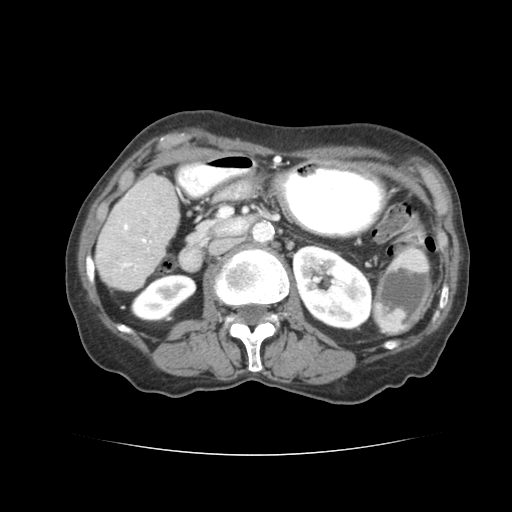
Contrast-enhanced abdominal CT (liver protocol), one axial slice; slice 20 of 77 in the series (ordered by position); reconstruction kernel STANDARD; 120 kVp; soft-tissue window (W 400 / L 40 HU); 2.5 mm slice thickness; 512 × 512 image matrix. From the clinical record (not read from this slice): diagnosis: hepatocellular carcinoma (patient treated with transarterial chemoembolisation; whether this scan precedes or follows treatment is not stated here); TNM stage (as recorded): Stage-I; Child-Pugh class: A; tumour differentiation: well differentiated.
Annotated regions visible in this slice (semi-automatic segmentation, software-assisted and operator-edited):
- liver parenchyma outside the tumour (the mass and vessels are separate outlines, so this box may not span the whole liver): box from (x=94, y=172) to (x=176, y=288) px
- liver vessels: (x=121, y=191)–(x=159, y=264)